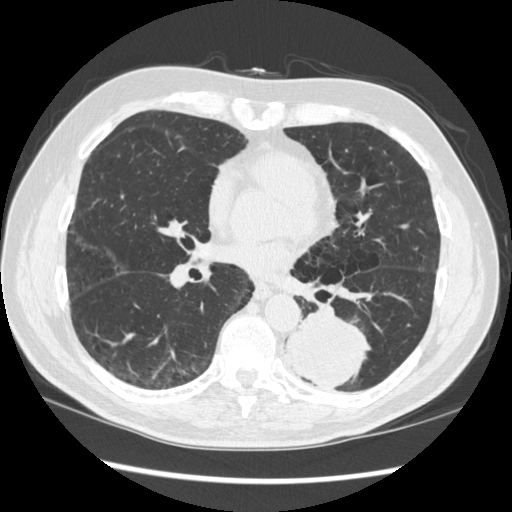
Axial slice from a low-dose chest CT screening exam. First (baseline) screen. Lung window (W 1500 / L -600 HU). Standard (soft-tissue) reconstruction kernel (STANDARD). Slice 151 of 348 in the series. 512 × 512 image matrix, field of view 360 × 360 mm. Male participant, aged 72 years at enrolment. Current smoker at enrolment.
Expert reader's lesion annotation, bounding box <267,303,371,394> (left, top, right, bottom; pixels). The screening reader recorded 2 non-calcified nodules or masses ≥4 mm on this exam; which of them this box marks is not recorded. Official screen result: positive, change unspecified: nodule(s) >= 4 mm or enlarging nodule(s), mass(es), or other non-specific abnormalities suspicious for lung cancer. Lung cancer was diagnosed 37 days after this screen: squamous cell carcinoma, NOS, left lower lobe, stage IIIA (AJCC 6th edition), 60 mm at pathology.